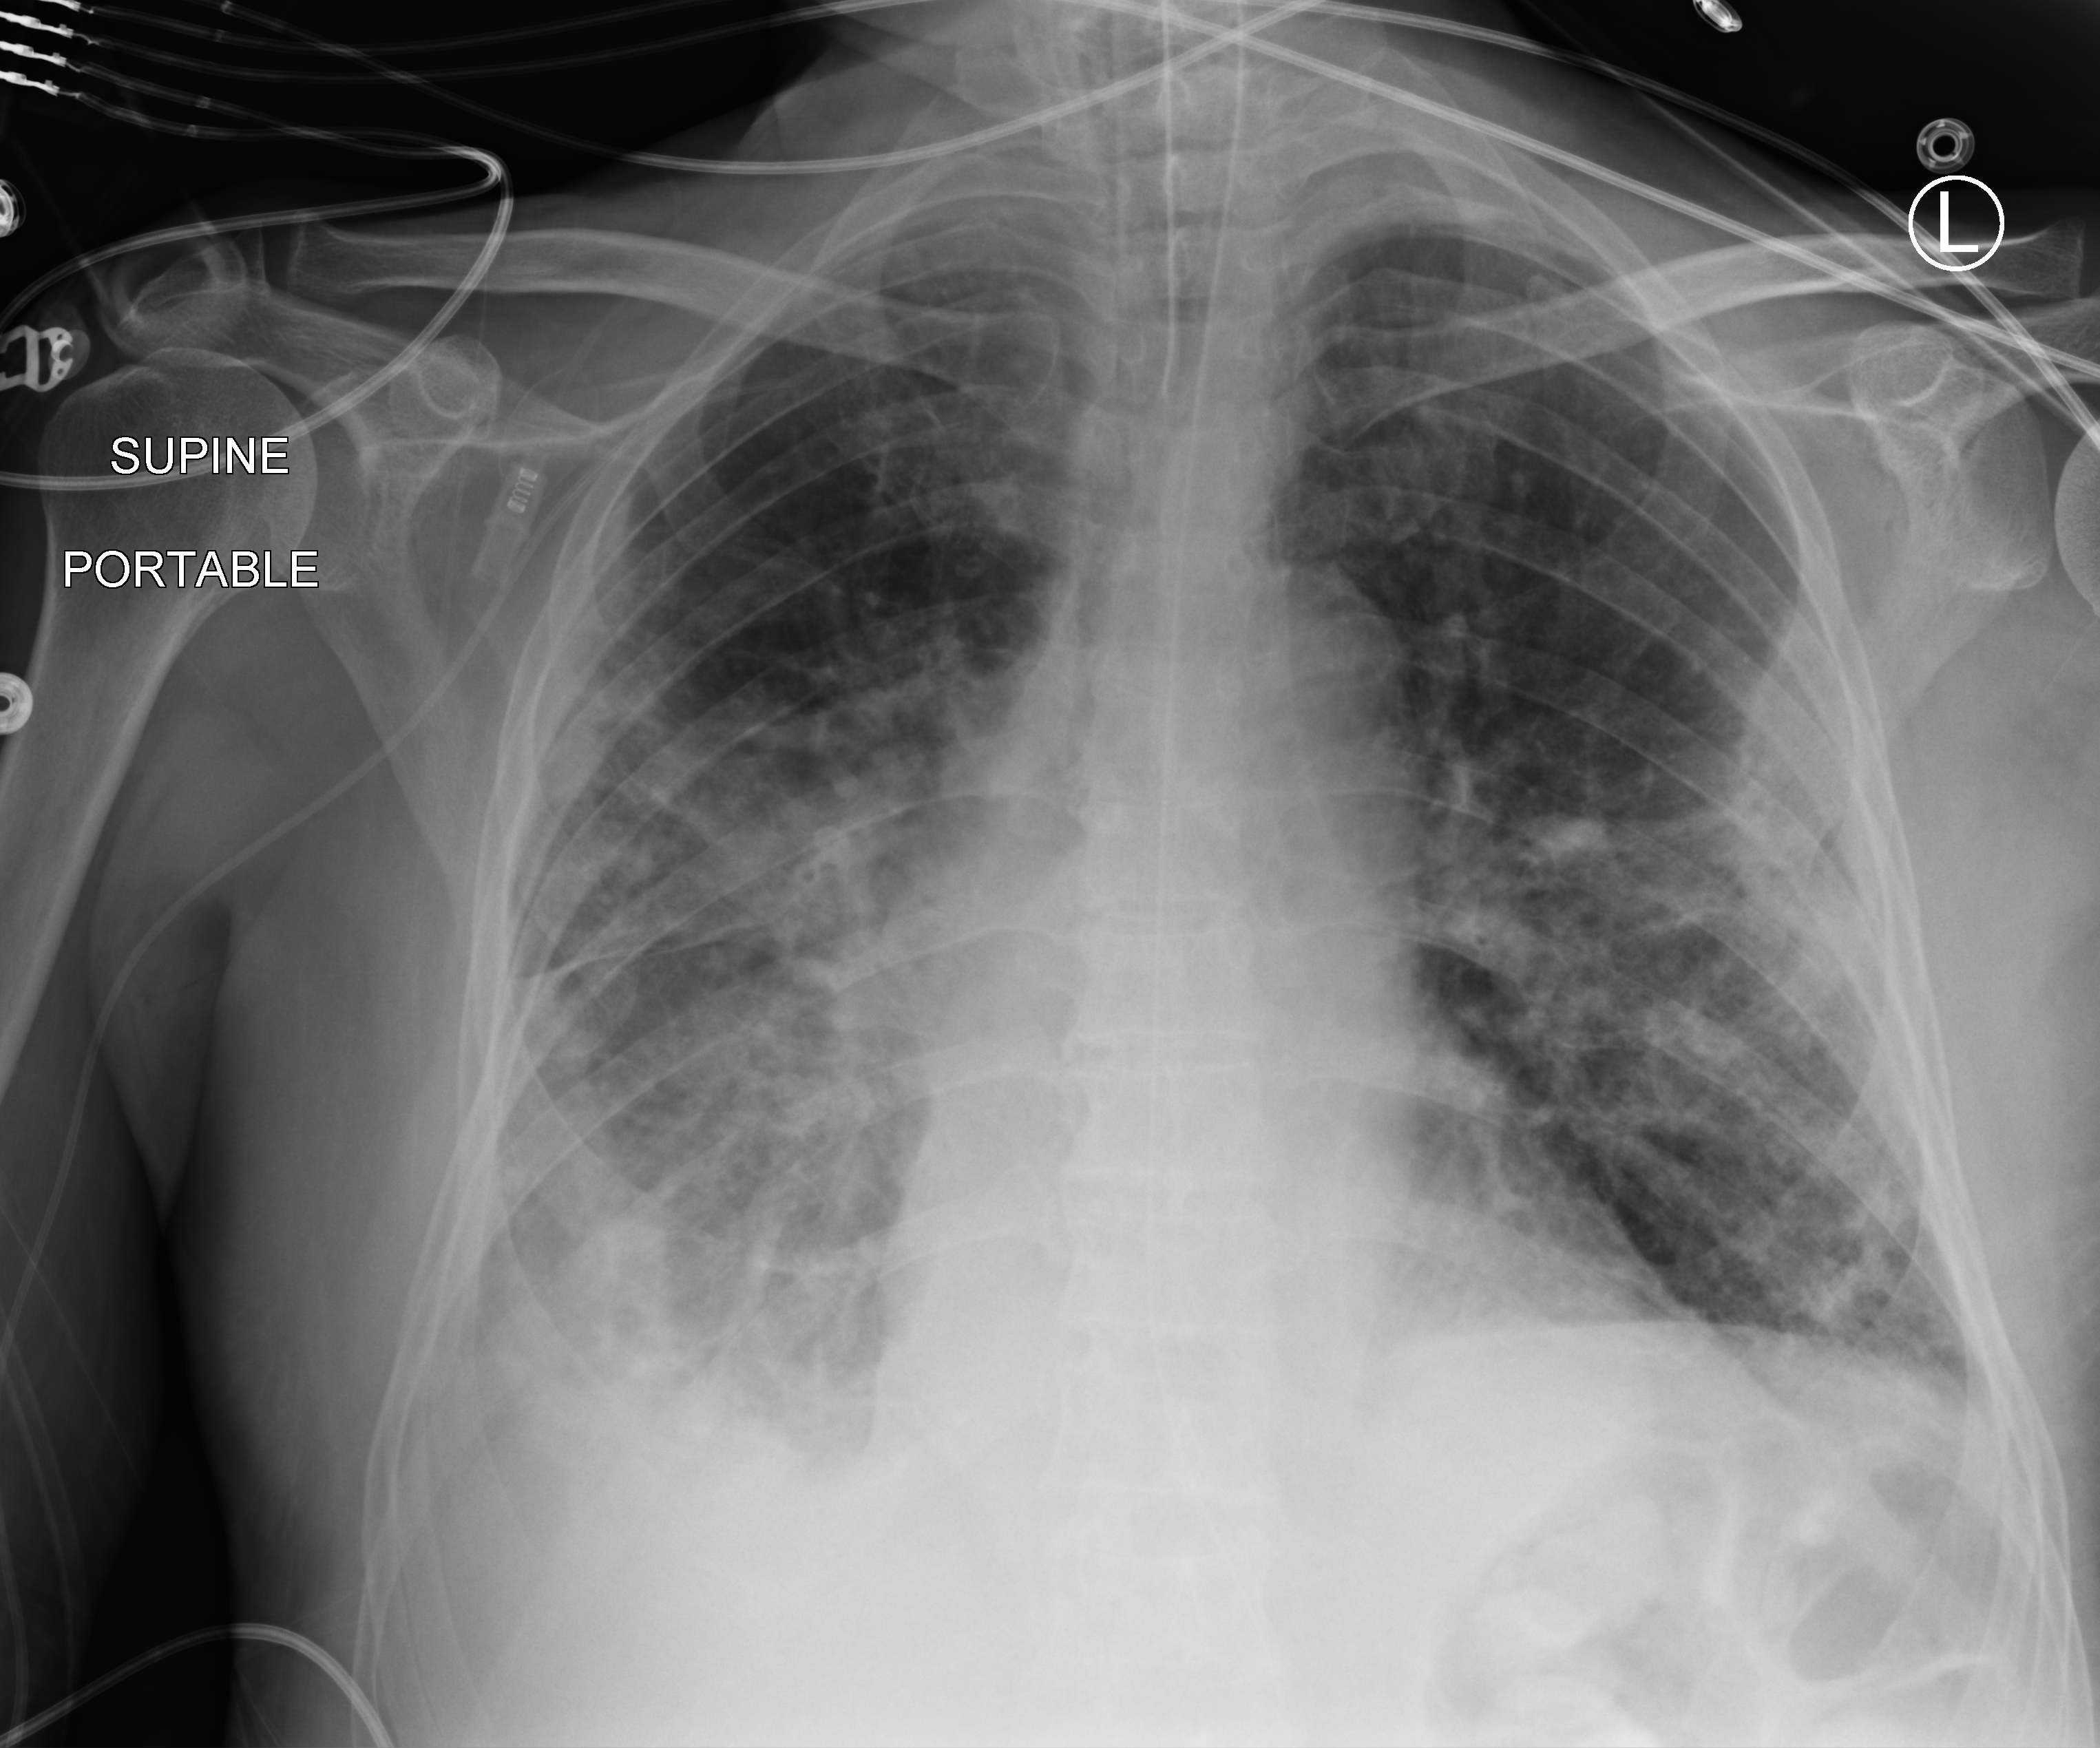
Bedside chest radiograph (computed radiography), anteroposterior (AP) projection. Male patient hospitalised with COVID-19, age 75–90 years.
From the hospital-stay record, not from the radiograph (when in the stay this image was taken is not recorded): chronic kidney disease (admission record): no.